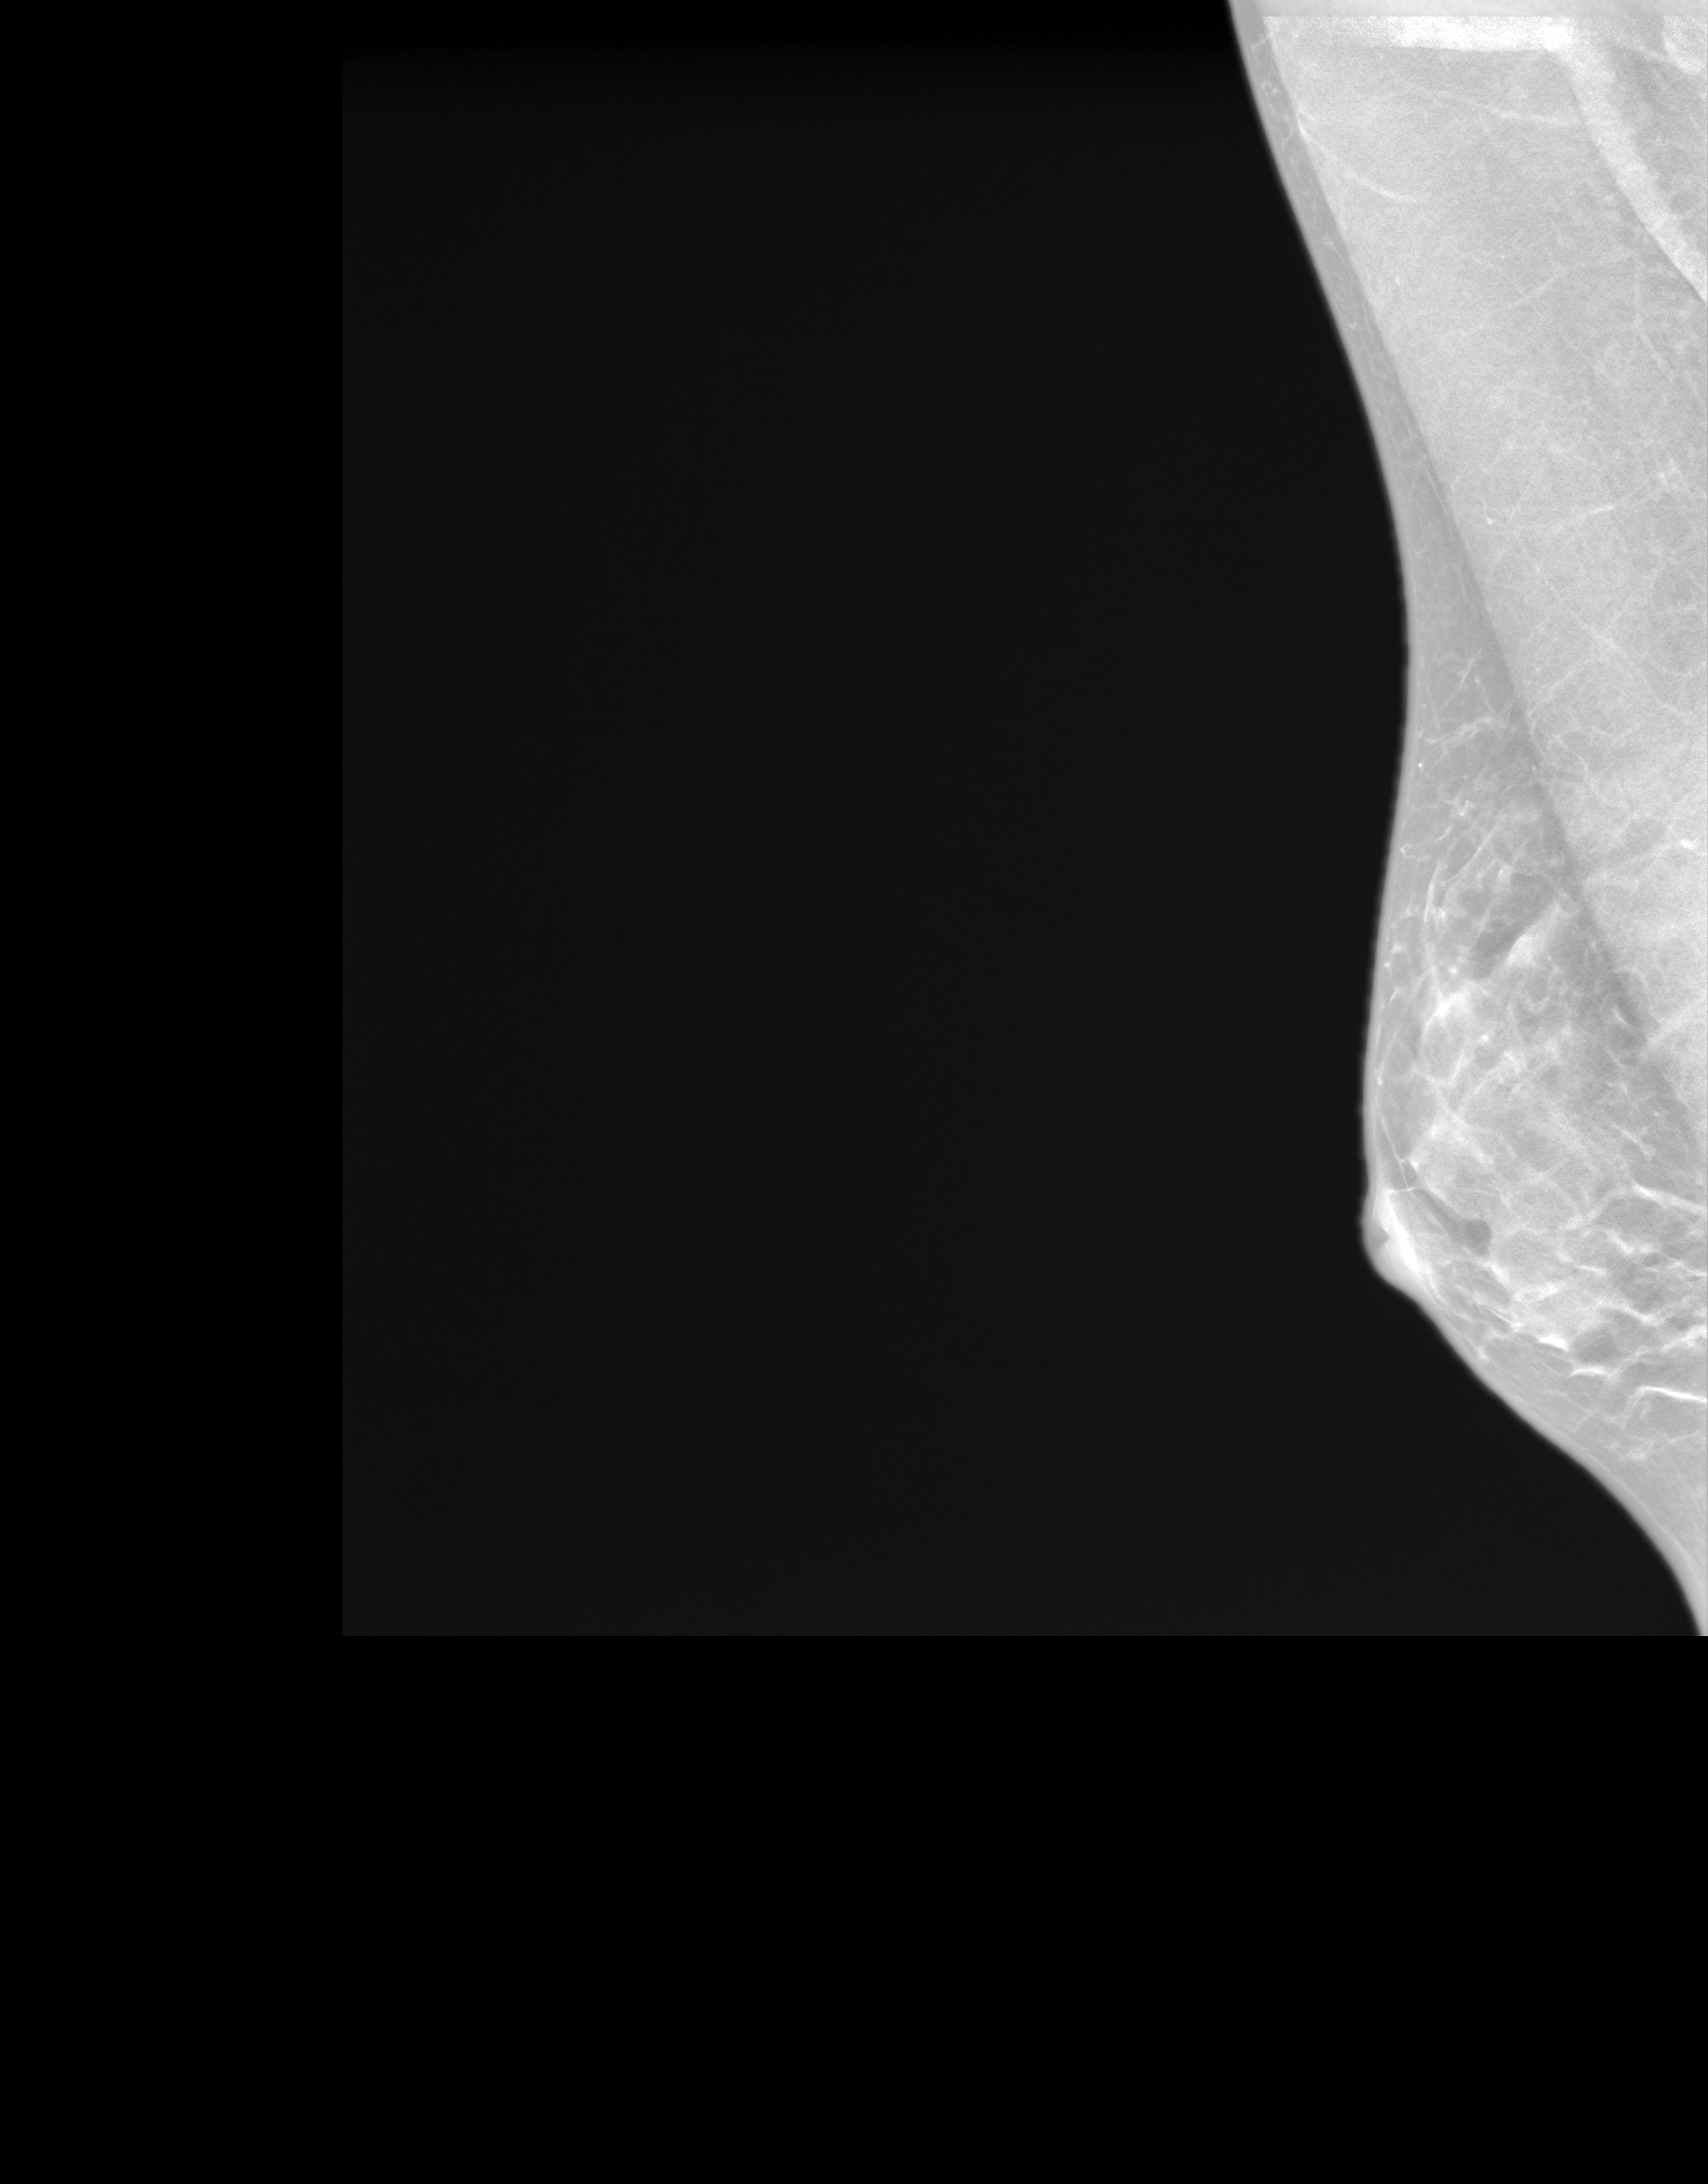
Screening examination; system: SenoIris_1SP2(440). Patient aged 56 years (female).
Image type: synthesized 2-D view from tomosynthesis. Breast: right. Projection: mediolateral oblique (MLO) view.